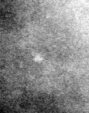
Region of interest cut from a scanned film mammogram (one marked finding), left breast, MLO view.
Marked abnormality: calcifications, morphology amorphous / round and regular, distribution clustered; BI-RADS assessment category 4; pathology (as recorded): malignant.